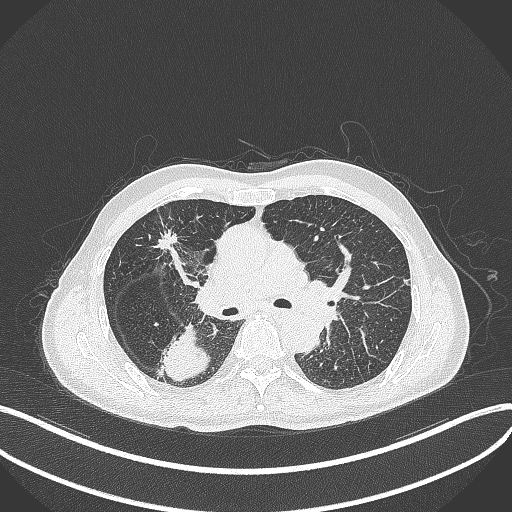
Chest CT, one axial slice. Position 273 of 428 along the scan axis. Lung window (W 1500 / L -600 HU). 512 × 512 image matrix. Patient: male, 79 years. Case-level facts recorded for this patient, not image findings: clinical TNM (as recorded): T3 N0 M0.
Structures marked on this image (rectangle marked by the reading radiologist):
- lung tumour (recorded histology: adenocarcinoma): bounding box (x1, y1, x2, y2) in pixels: (161, 323, 210, 384)